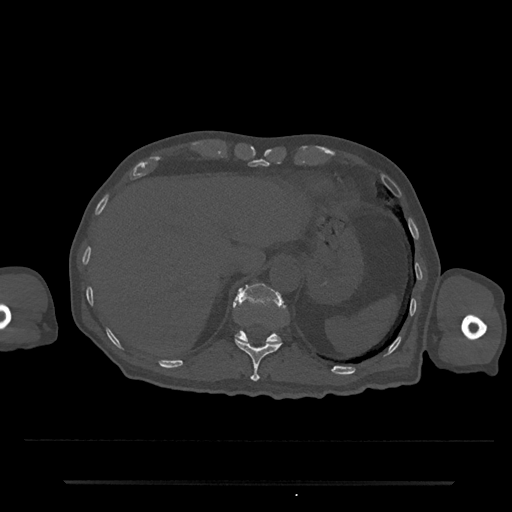
CT including the spine, one axial slice. Slice 235 of 797 in the series (ordered by position). 120 kVp. Bone window (W 1800 / L 400 HU). 0.5 mm slice thickness. 512 × 512 image matrix, field of view 427 × 427 mm. Male patient, age 74 years. Case-level facts recorded for this patient, not image findings: primary cancer: prostate.
Structures marked on this image (semi-automatically segmented with operator editing):
- T11 vertebra: box from (x=234, y=338) to (x=282, y=382) px
- T12 vertebra: (x=236, y=283)–(x=282, y=344)